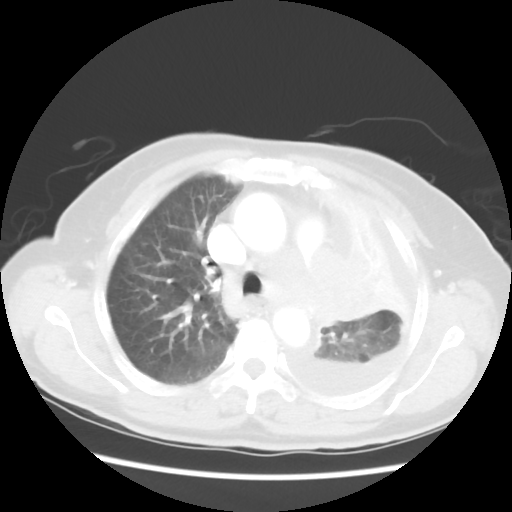
Chest CT, one axial slice; slice 37 of 52 in the series (ordered by position); 120 kVp; lung window (W 1500 / L -600 HU); 5 mm slice thickness; 512 × 512 image matrix, field of view 336 × 336 mm. Female patient, age 72 years. Case-level facts recorded for this patient, not image findings: clinical TNM (as recorded): T4 N3 M1b.
Structures marked on this image (rectangle marked by the reading radiologist):
- lung tumour (recorded histology: large cell carcinoma): bounding box [x1, y1, x2, y2] px = [301, 248, 381, 326]